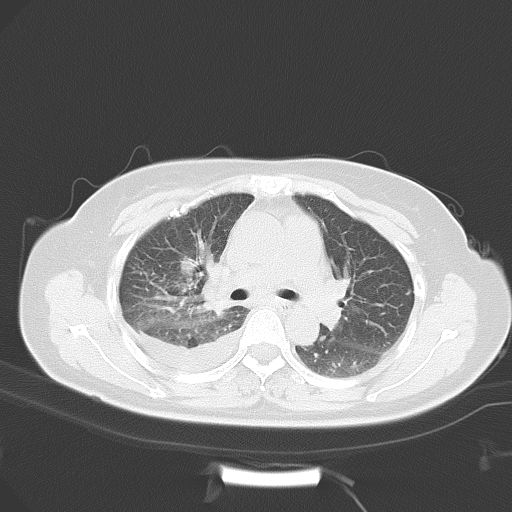
Chest CT, one axial slice. Position 23 of 41 along the scan axis. Lung window (W 1500 / L -600 HU). 5 mm slice thickness. 512 × 512 image matrix, field of view 360 × 360 mm. Patient: female, 53 years. Case-level facts recorded for this patient, not image findings: clinical TNM (as recorded): T1c N1 M1b.
Structures marked on this image (rectangle marked by the reading radiologist):
- lung tumour (recorded histology: adenocarcinoma): box from (x=176, y=253) to (x=201, y=280) px